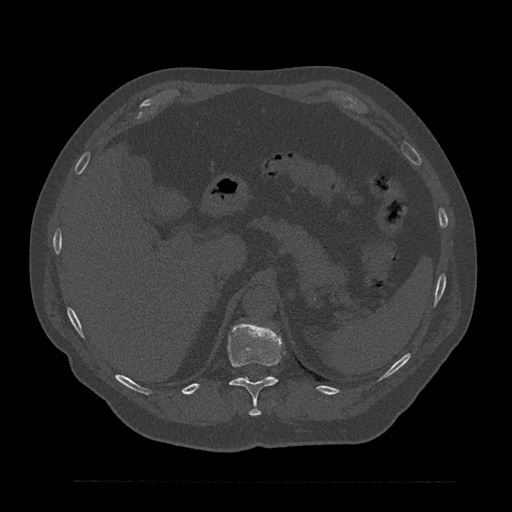
CT including the spine, one axial slice; slice 282 of 797 in the series (ordered by position); reconstruction kernel Br40s/3; 120 kVp; bone window (W 1800 / L 400 HU); 512 × 512 image matrix, field of view 430 × 430 mm. Male patient, age 61 years. Case-level facts recorded for this patient, not image findings: primary cancer: prostate.
Annotated regions visible in this slice (semi-automatically segmented with operator editing):
- T11 vertebra: bounding box (x1, y1, x2, y2) in pixels: (227, 323, 282, 416)